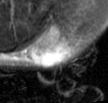
MRI of an extremity soft-tissue mass, one axial slice. Slice 30 of 42 in the series (ordered by position). T2-weighted fat-saturated. MR volume resampled by the dataset authors to the PET/CT grid (not the native acquisition matrix). 3.27 mm slice thickness. 108 × 103 image matrix. Male patient. Case-level facts recorded for this patient, not image findings: histological type: leiomyosarcoma; grade: intermediate; site of the primary tumour: left pelvis.
Outlined on this slice (expert contour drawn on MRI and transferred to this co-registered scan by the dataset authors):
- gross tumour volume (mass): bounding box [x1, y1, x2, y2] px = [28, 21, 81, 68]